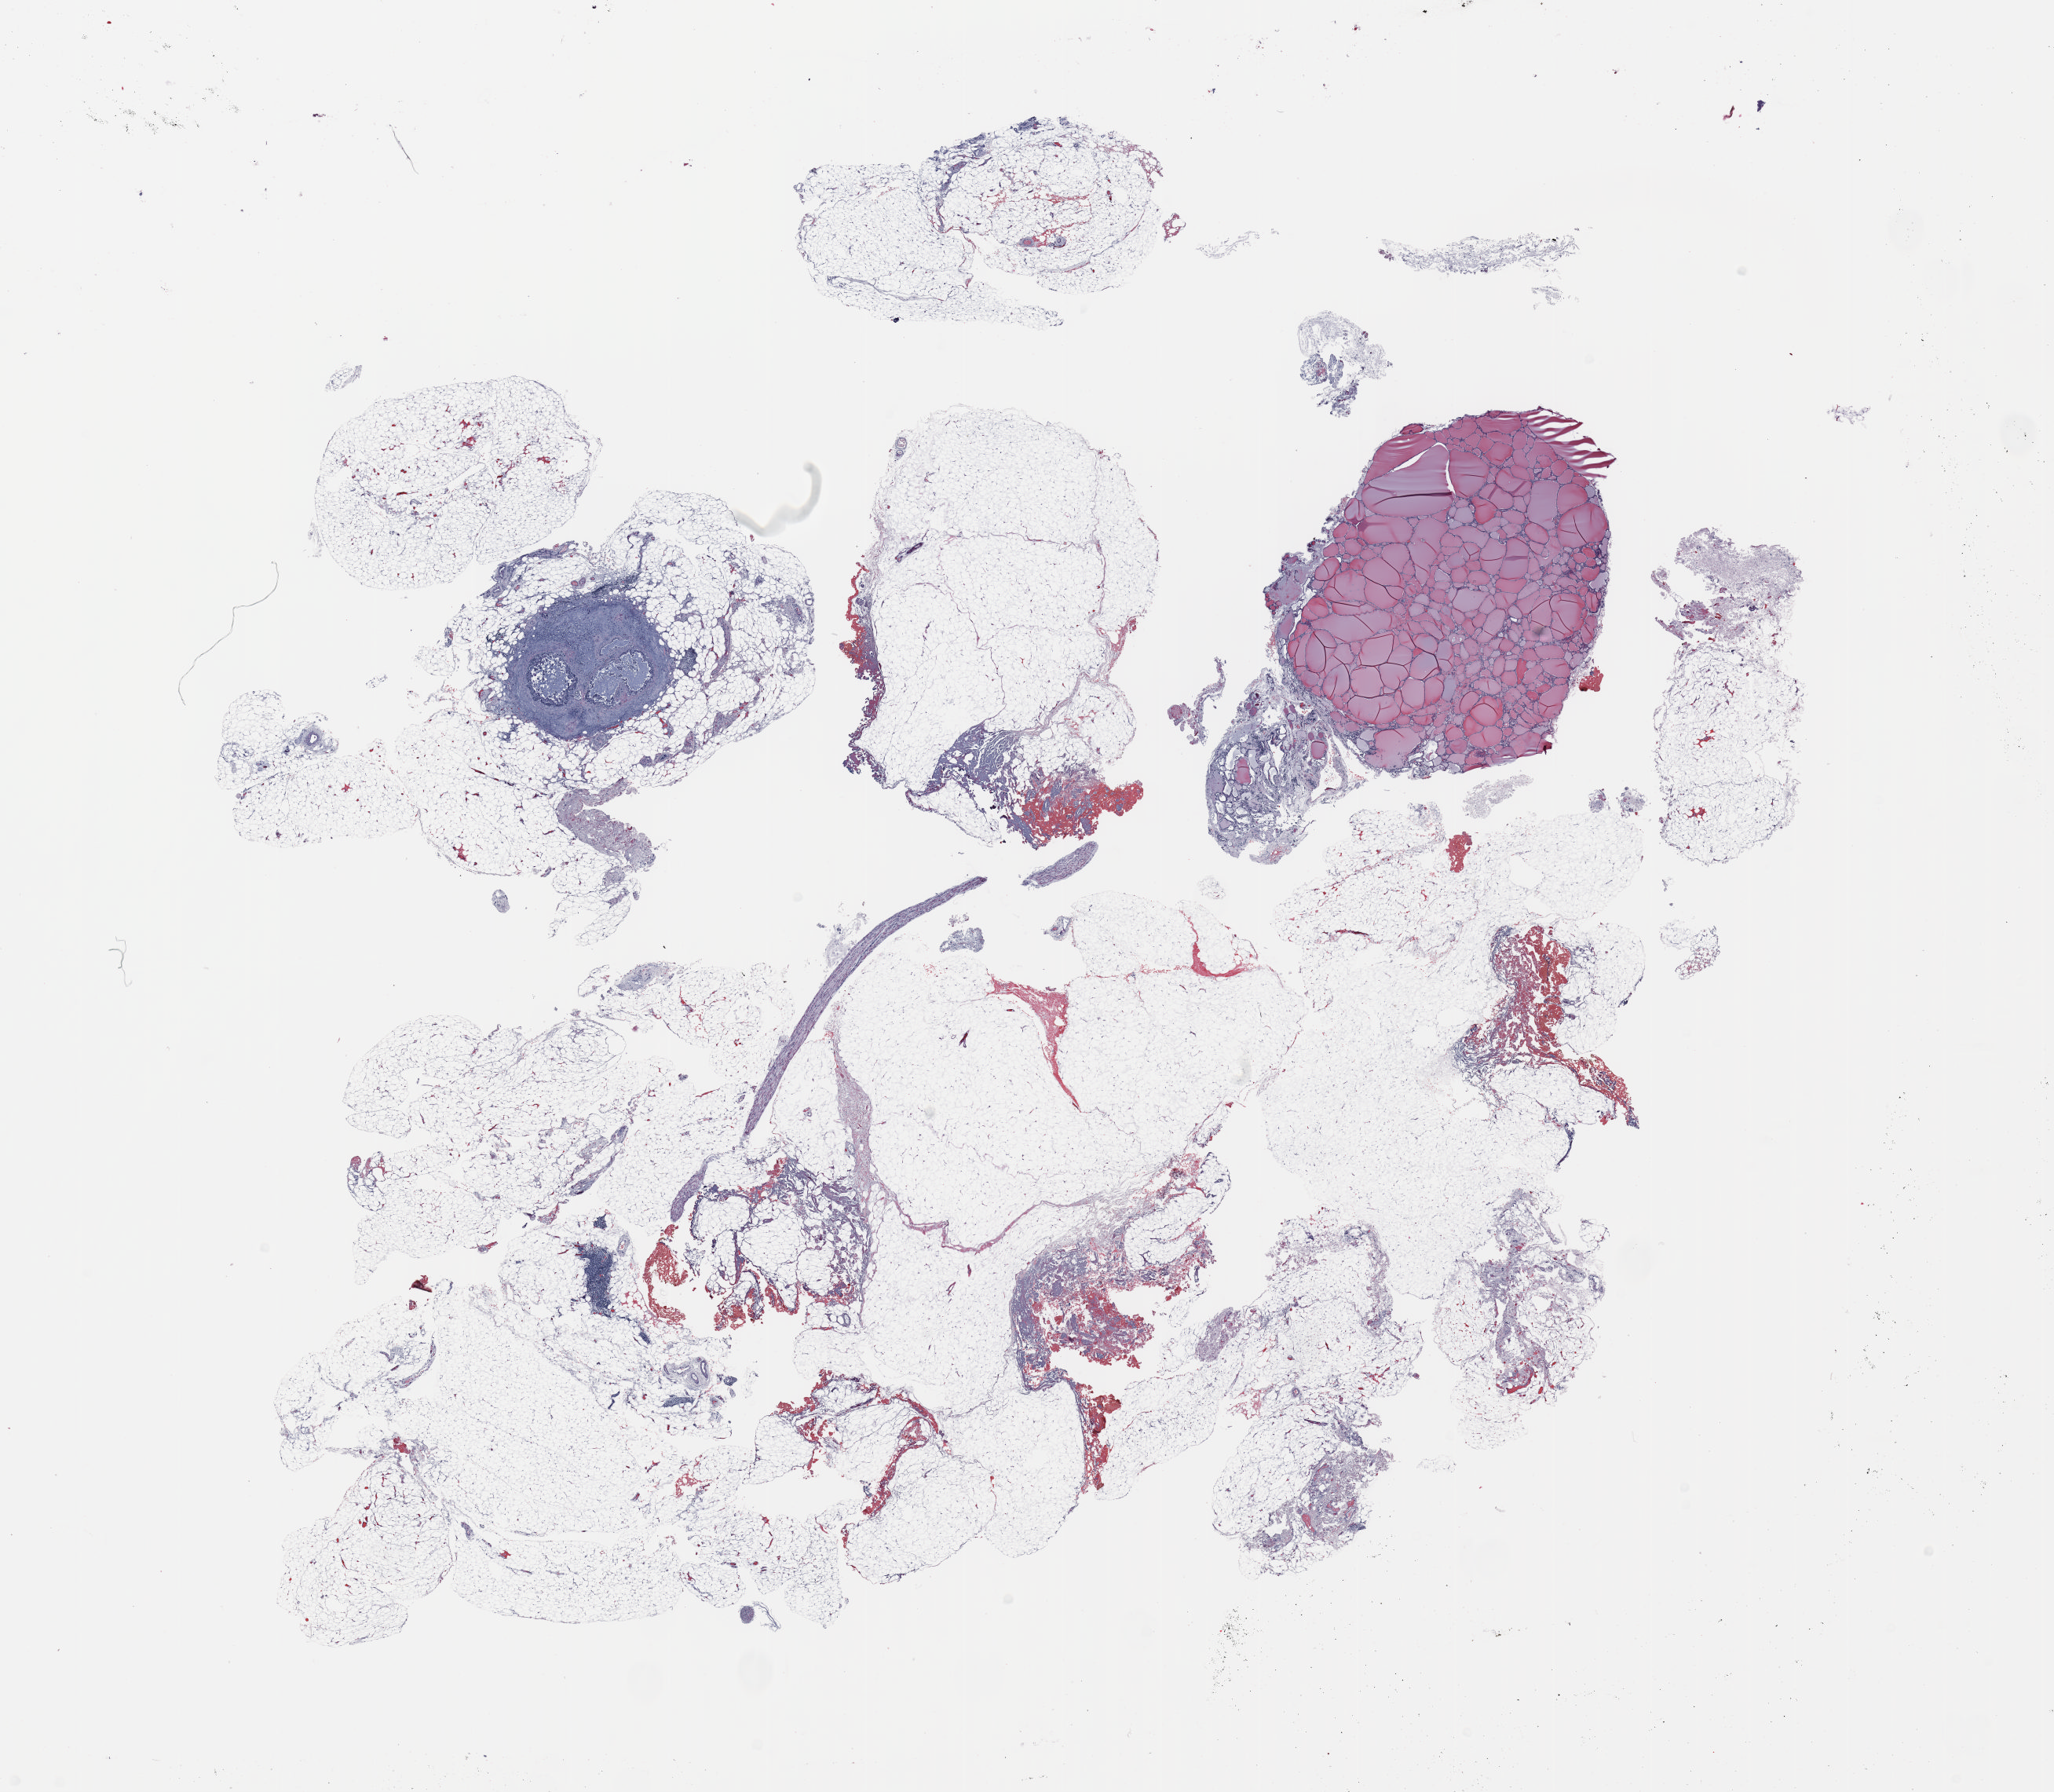
Whole-slide histology image, H&E — shown as a low-resolution overview of the whole scanned area (about 21.0 x 18.3 mm). Formalin-fixed paraffin-embedded (FFPE) section. Lung tissue. Male, age 70 at enrolment. Grade: cannot be assessed (GX).
Stage (AJCC 6th edition): IV. Participant's lung-cancer diagnosis: Adenocarcinoma, NOS.